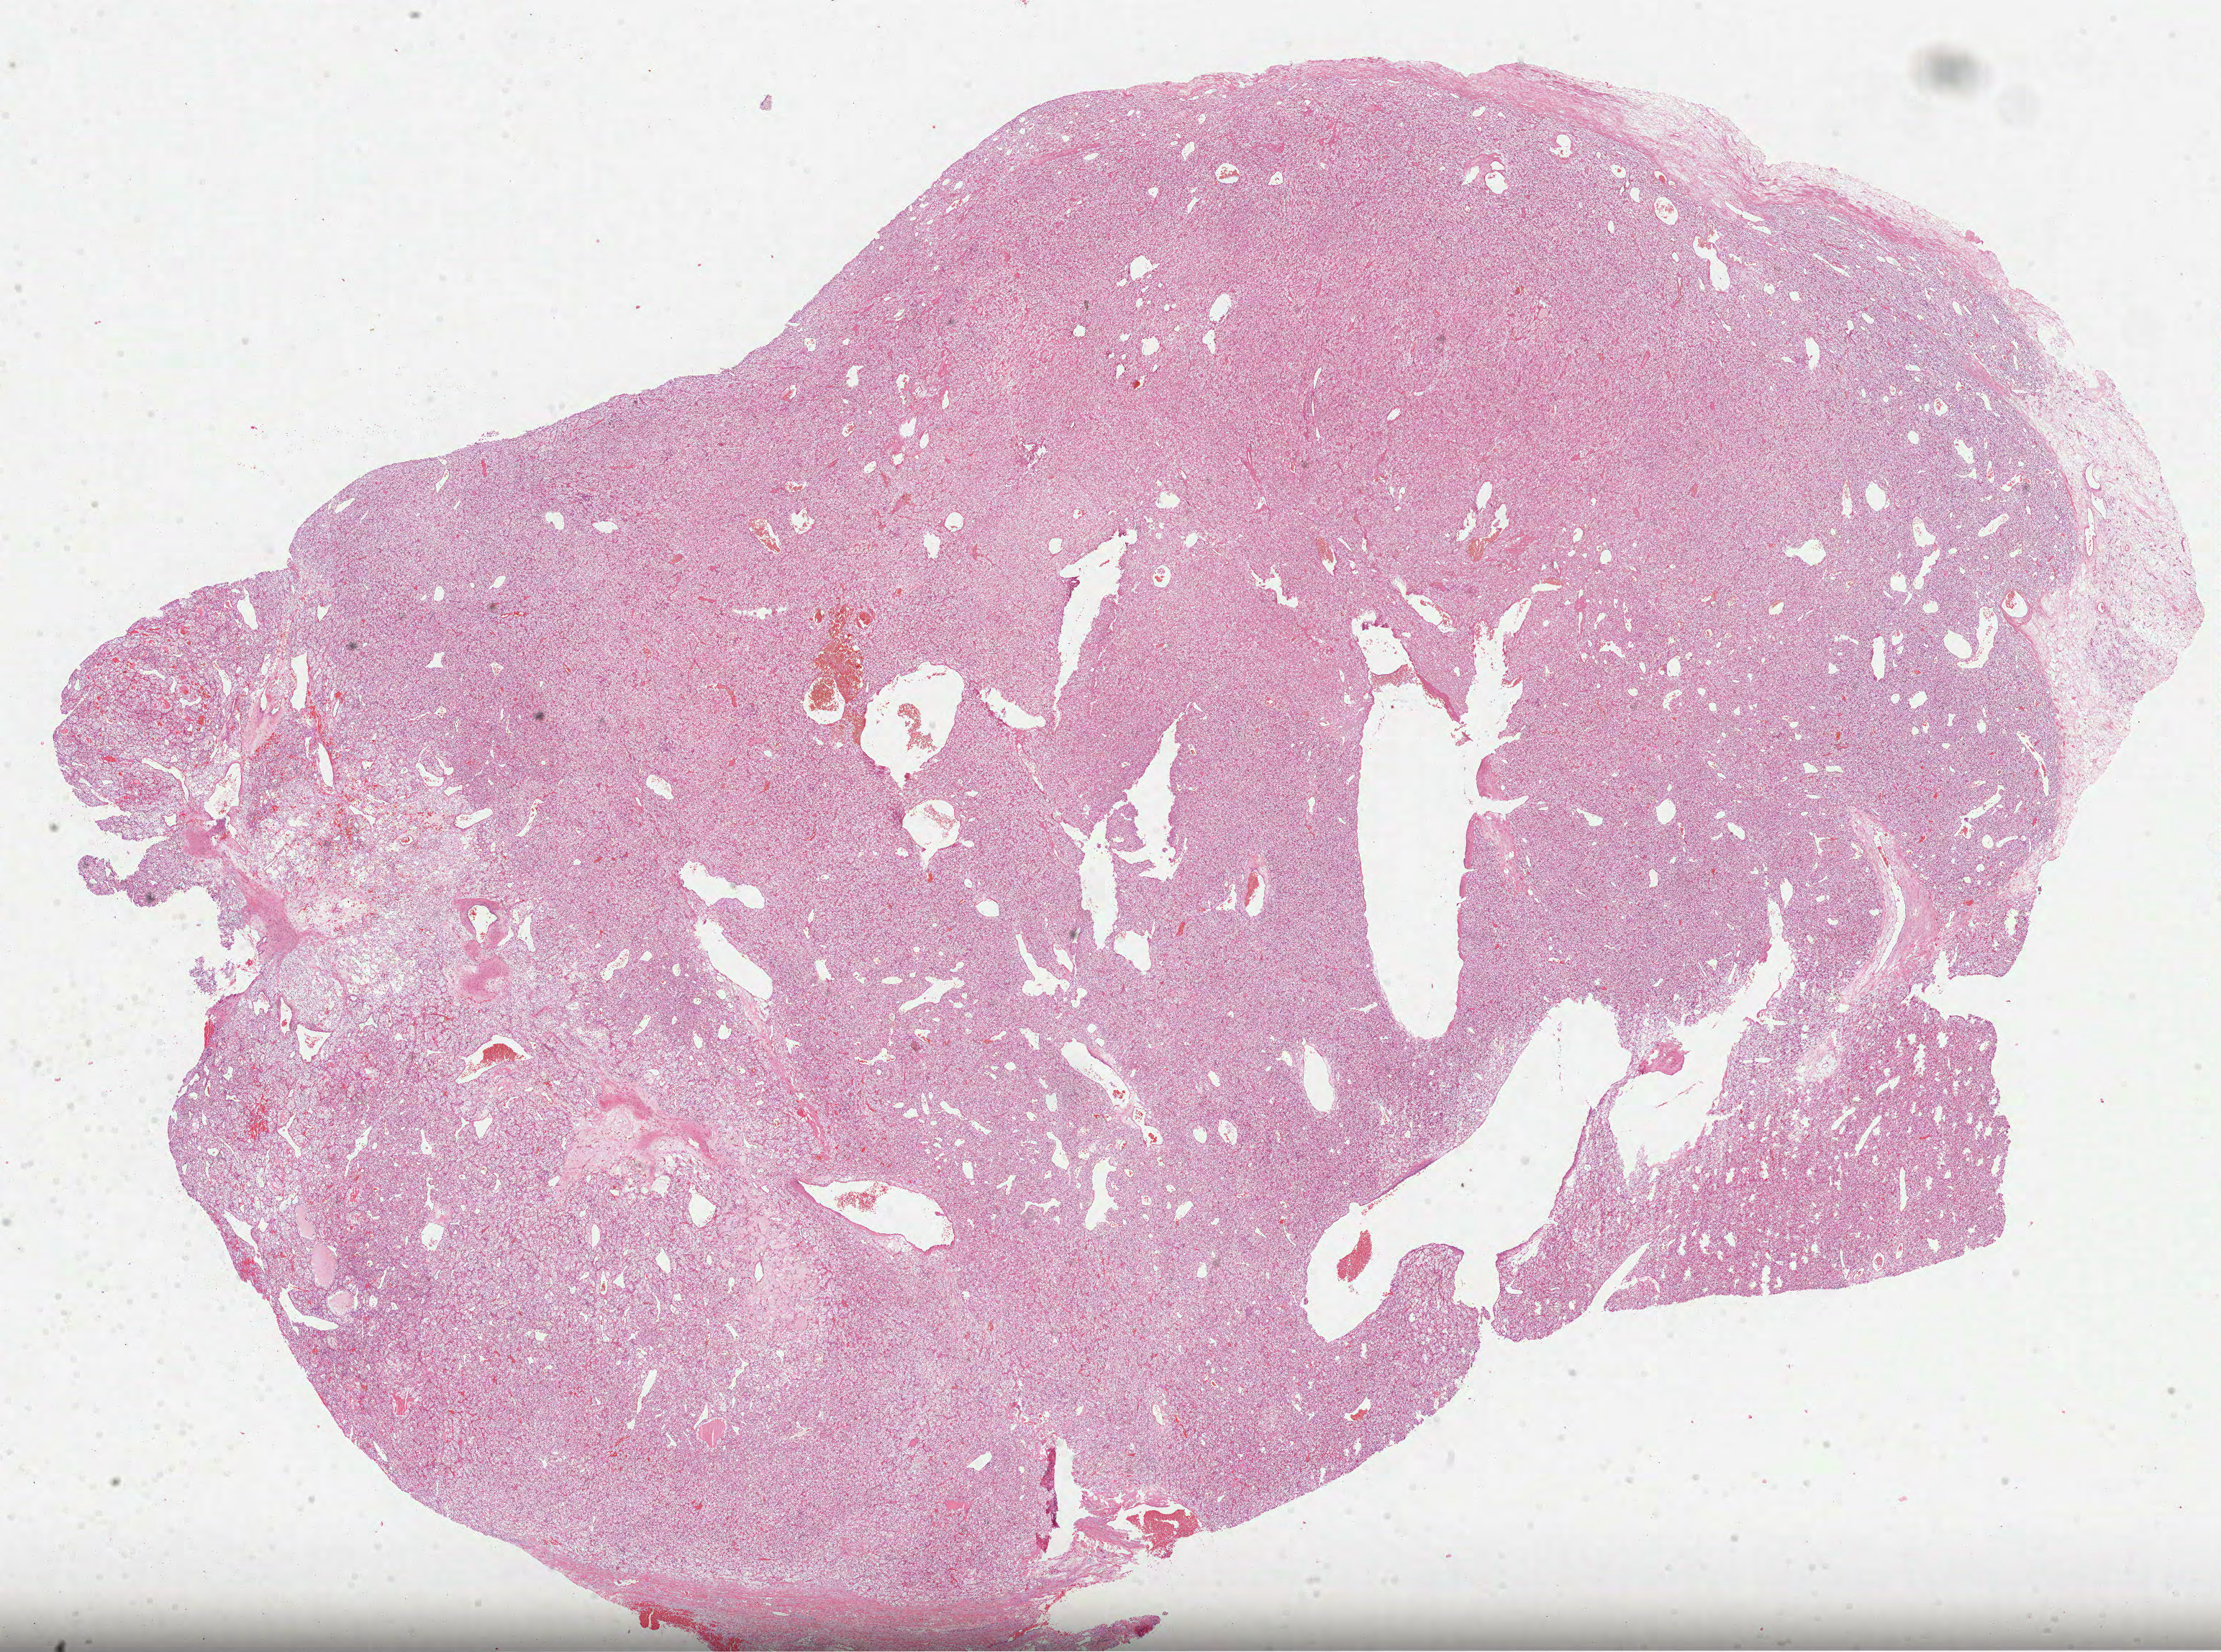
H&E-stained whole-slide image — a low-resolution overview of the entire scanned area, about 24.9 x 18.5 mm, formalin-fixed paraffin-embedded (FFPE) diagnostic section, kidney, primary tumour sample. Male patient; age at initial diagnosis 79 years. Histologic grade: G3 (poorly differentiated).
• AJCC pathologic stage: II
• laterality: left
• diagnosis: Clear cell adenocarcinoma, NOS
• lymph nodes positive (case pathology): 0 of 1 examined